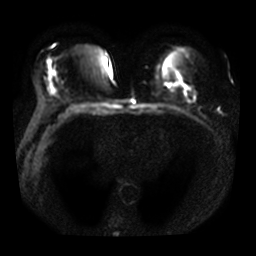
Breast MRI, one axial slice. Position 16 of 32 along the scan axis. Diffusion-weighted series; image 2 of 4 stored at this slice position (different b-values; order by instance number). 3 T. 256 × 256 image matrix. Female patient.
Outlined on this slice (manually delineated by an expert):
- tumour on diffusion-weighted imaging: bounding box [x1, y1, x2, y2] px = [182, 86, 185, 91]